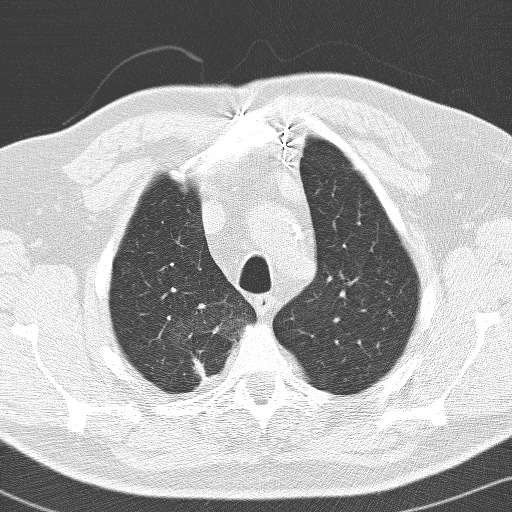
Chest CT (low-dose screening protocol), one axial image. Baseline annual screen. Lung window (W 1500 / L -600 HU). 3.2 mm slice thickness. Lung (sharp) reconstruction kernel (D). Slice 23 of 141 in the series. Male, age 66 years at enrolment. Former smoker at enrolment.
- Expert reader's lesion annotation, bounding box (x1, y1, x2, y2) in pixels: (156, 321, 230, 394).
- The exam's reader record, not a measurement of the box and not confirmed to be the same lesion: non-calcified nodule or mass ≥4 mm, right upper lobe, 36 × 30 mm, spiculated (stellate) margins, soft tissue attenuation.
- Lung cancer was diagnosed 103 days after this screen: adenocarcinoma, NOS, right upper lobe, poorly differentiated (G3), stage IIB (AJCC 6th edition), 33 mm at pathology.